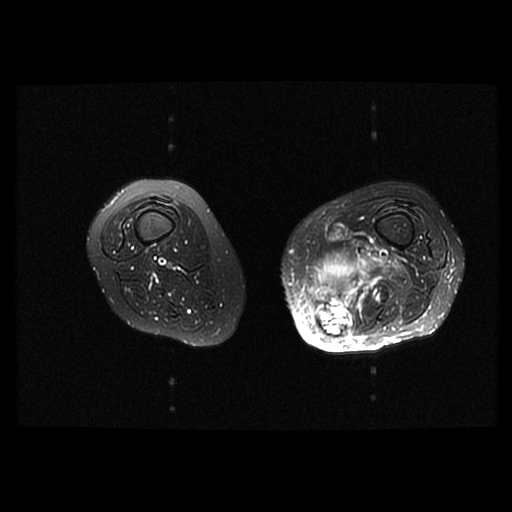
MRI of an extremity soft-tissue mass, one axial slice. Slice 23 of 42 in the series (ordered by position). T2-weighted fat-saturated. 512 × 512 image matrix, field of view 420 × 420 mm. Female patient. Case-level facts recorded for this patient, not image findings: histological type: pleomorphic leiomyosarcoma; grade: high; site of the primary tumour: left thigh.
Outlined on this slice (outlined manually by an expert reader):
- gross tumour volume including surrounding oedema: bounding box (x1, y1, x2, y2) in pixels: (306, 251, 400, 335)
- gross tumour volume (mass): (315, 297, 354, 335)